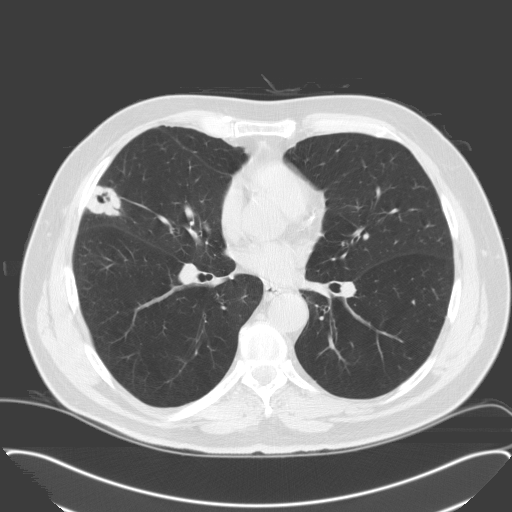
Low-dose screening chest CT, one axial slice. Slice 89 of 174 in the series (ordered by position). 120 kVp. Lung window (W 1500 / L -600 HU). 3.2 mm slice thickness. 512 × 512 image matrix.
Structures marked on this image (manually delineated by an expert):
- lesion 1 (tumor, middle lobe of right lung): box from (x=88, y=186) to (x=120, y=215) px